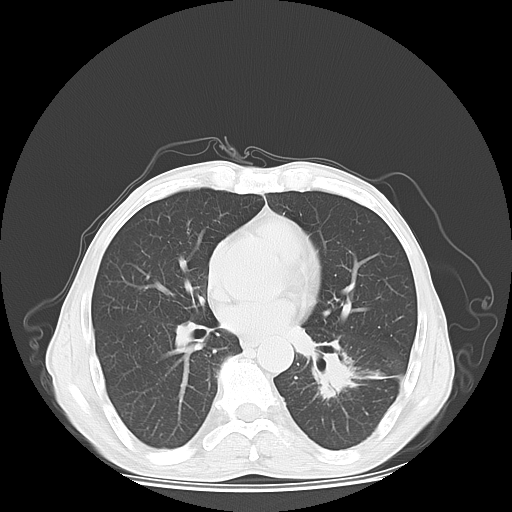
Chest CT, one axial slice; position 31 of 65 along the scan axis; reconstruction kernel LUNG; 120 kVp; lung window (W 1500 / L -600 HU); 5 mm slice thickness; 512 × 512 image matrix. Patient: male, 63 years. Case-level facts recorded for this patient, not image findings: clinical TNM (as recorded): T1c N0 M1b.
Structures marked on this image (rectangle marked by the reading radiologist):
- lung tumour (recorded histology: adenocarcinoma): bounding box (x1, y1, x2, y2) in pixels: (303, 344, 381, 407)